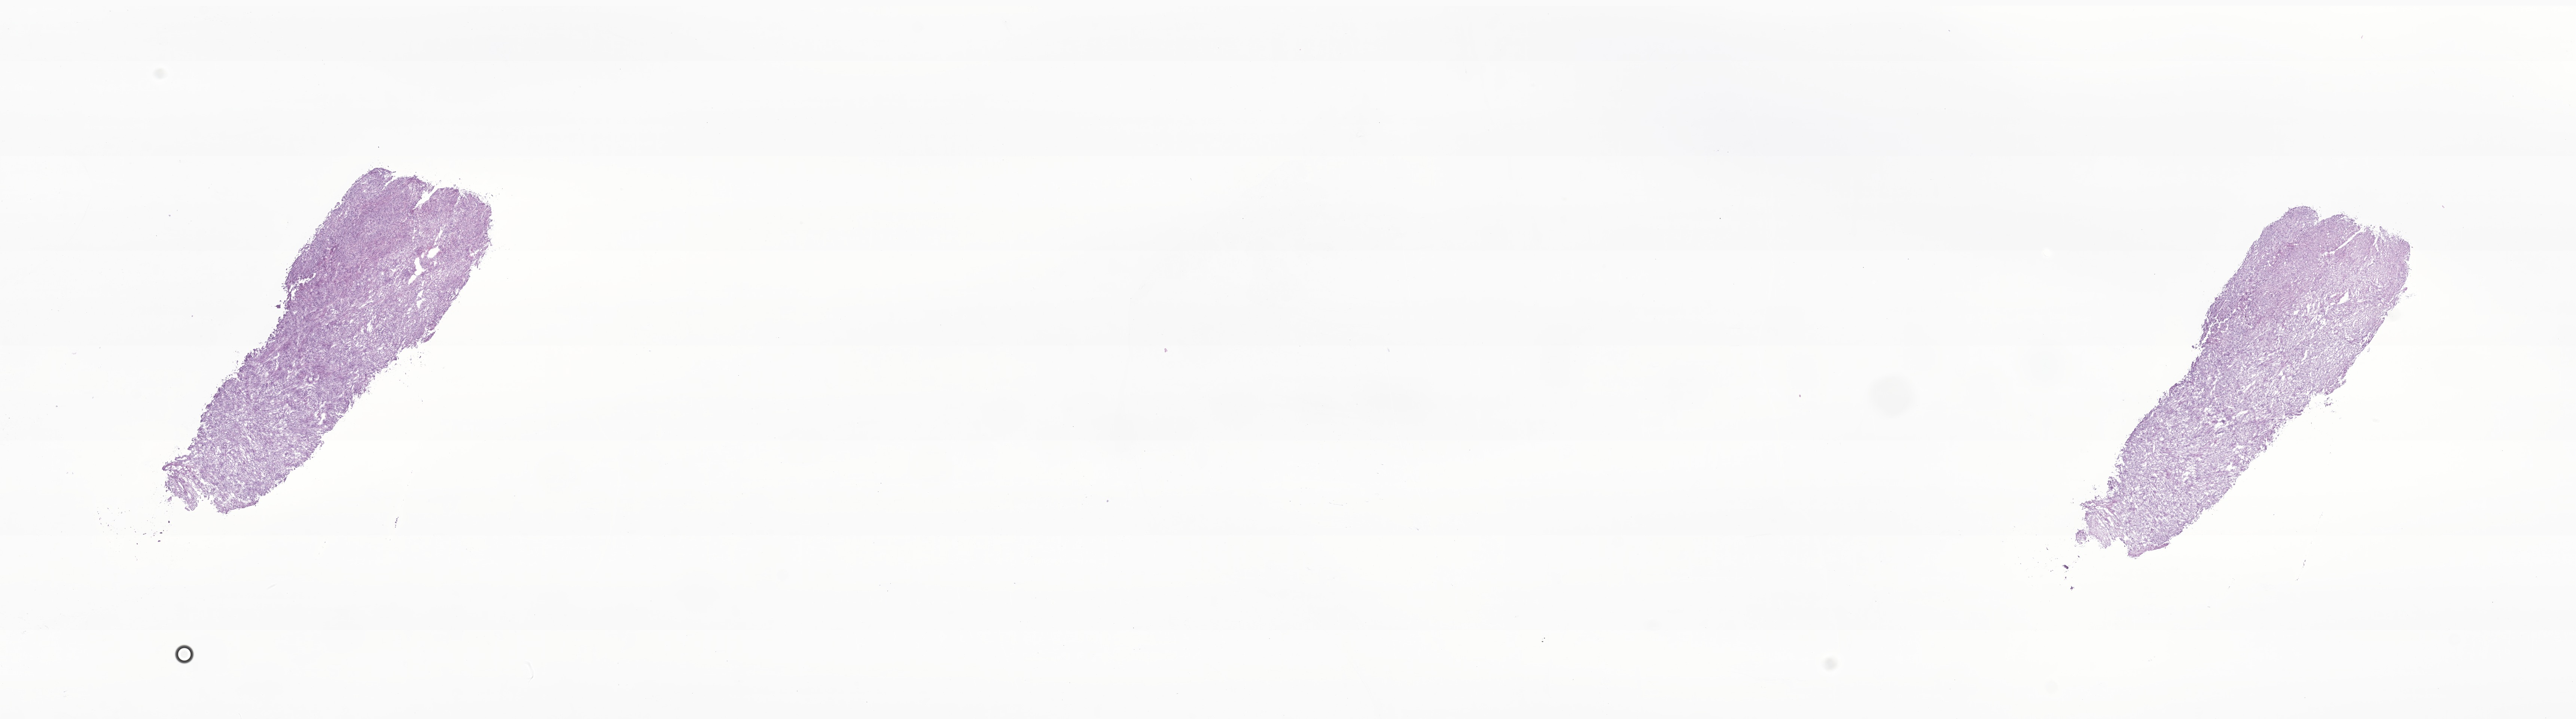
H&E whole-slide image of tumor tissue from the brain — whole scanned area (about 29.0 x 8.1 mm) shown as a low-resolution overview. Frozen section. Male patient, age 493 days.
Diagnosis: Atypical meningioma.